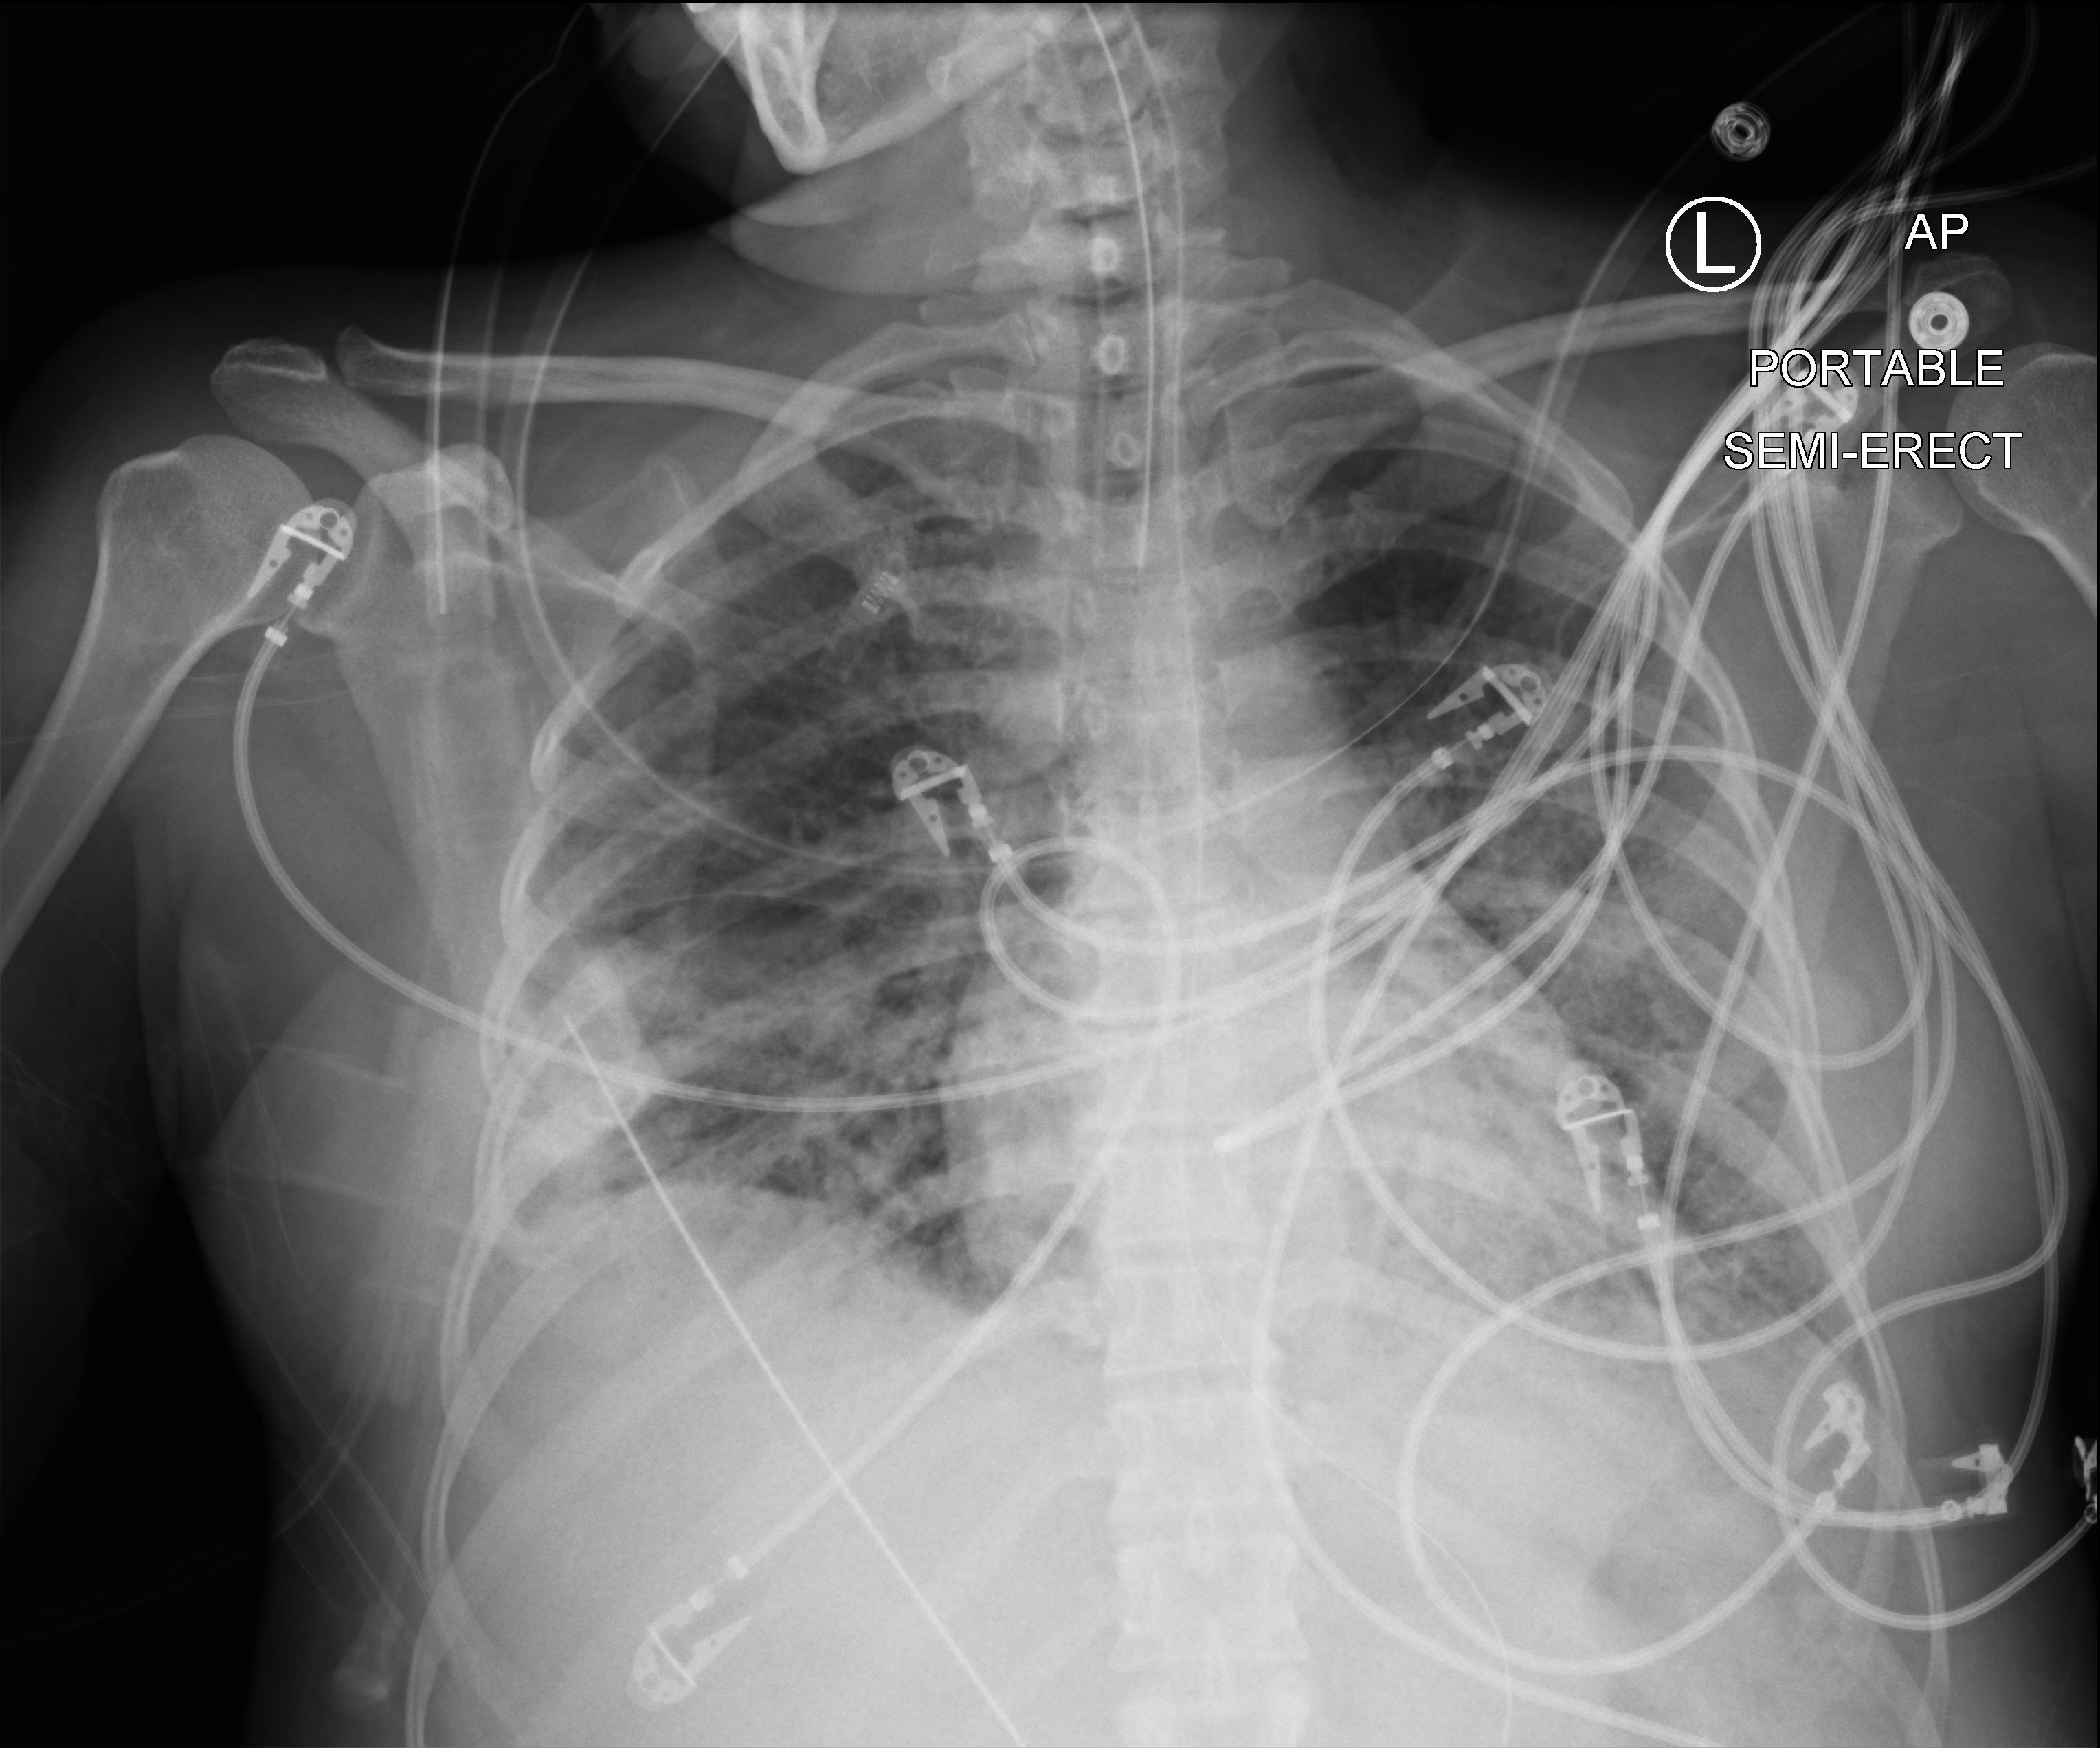
Chest X-ray (portable), anteroposterior (AP) projection. Female patient hospitalised with COVID-19, age 18–59 years.
From the hospital-stay record, not from the radiograph (when in the stay this image was taken is not recorded): mechanically ventilated during this hospital stay: yes; chronic kidney disease (admission record): no.